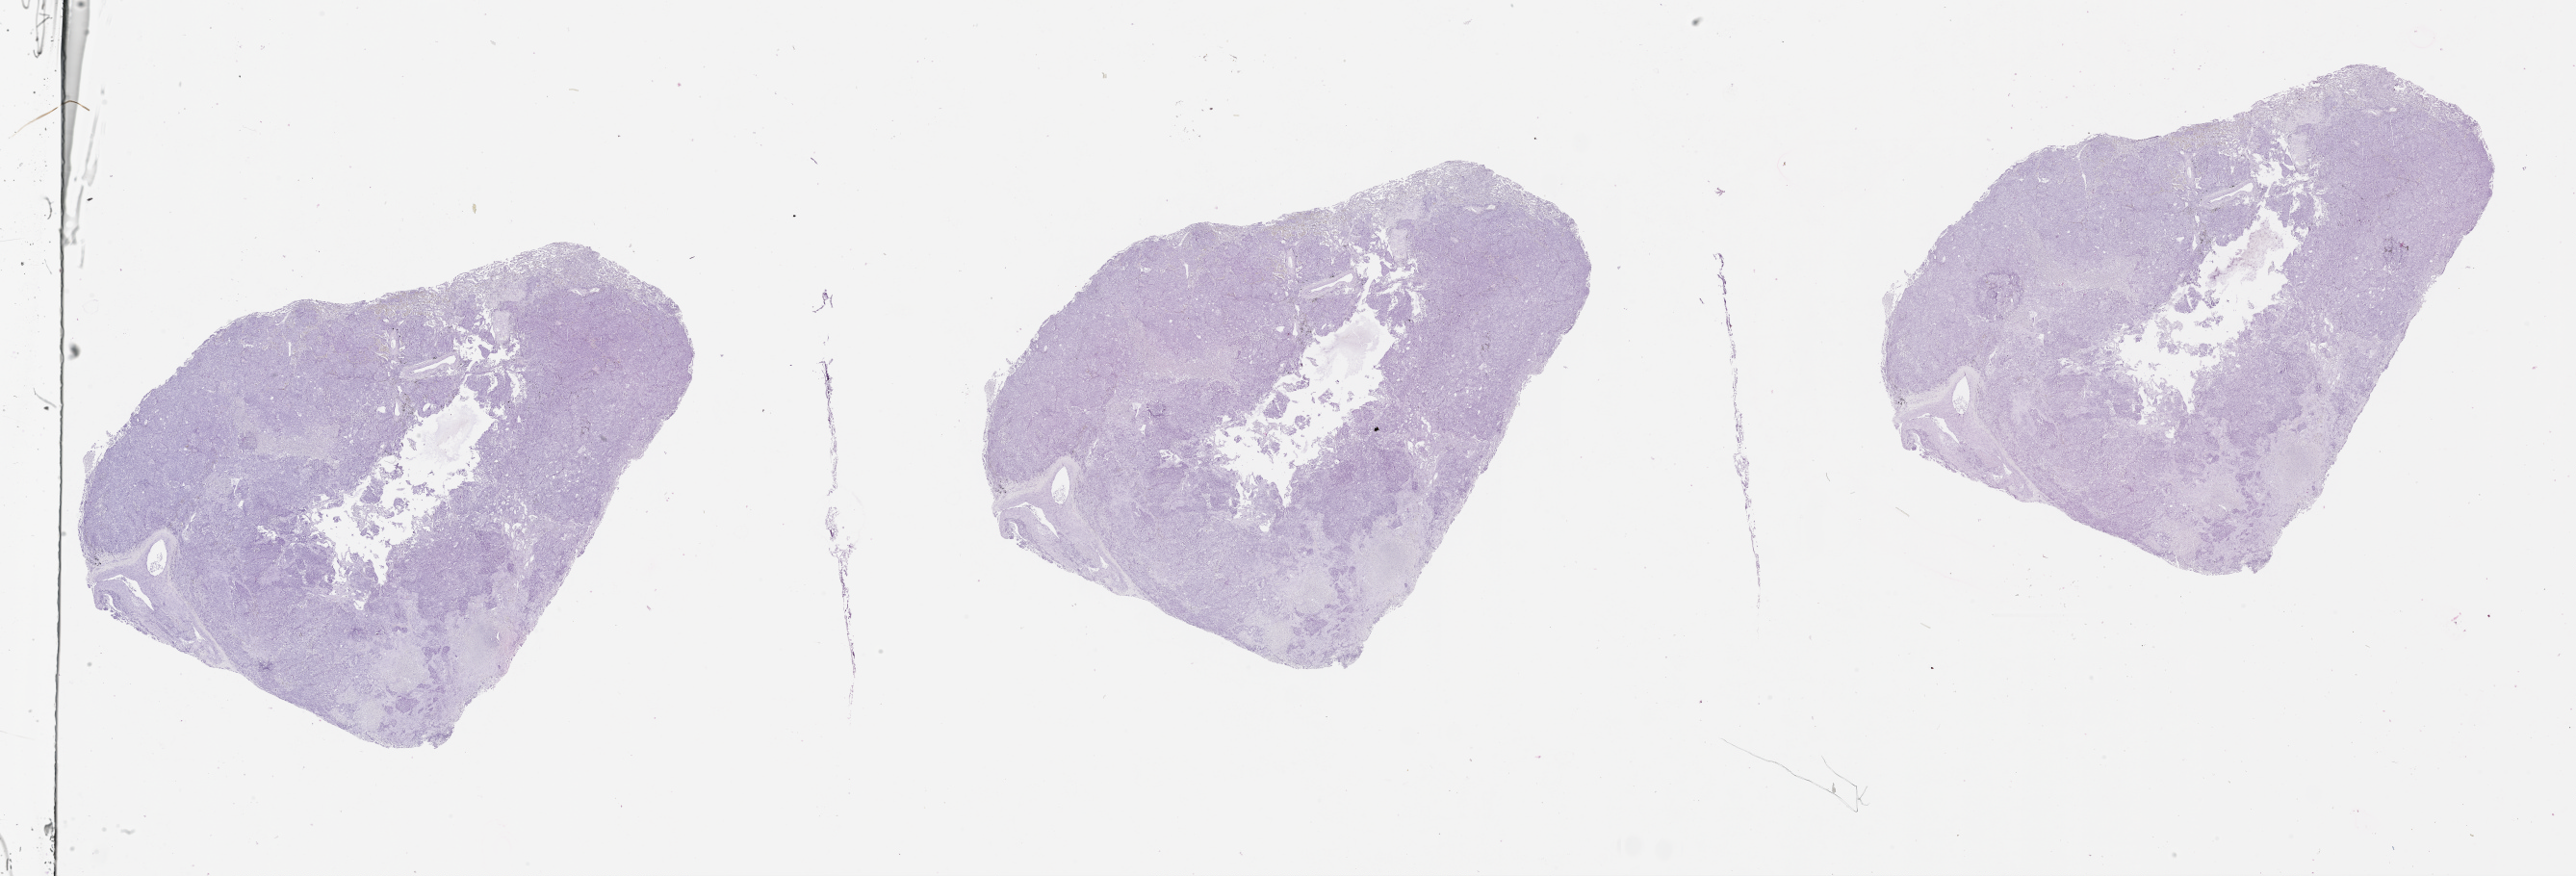
Digitized H&E-stained tissue section (whole slide) — low-resolution overview of the scanned area, about 43.1 x 14.7 mm (acquisition: 20x scan), lung, tissue type not recorded.
- patient diagnosis (cohort enrolment): lung adenocarcinoma (lung)